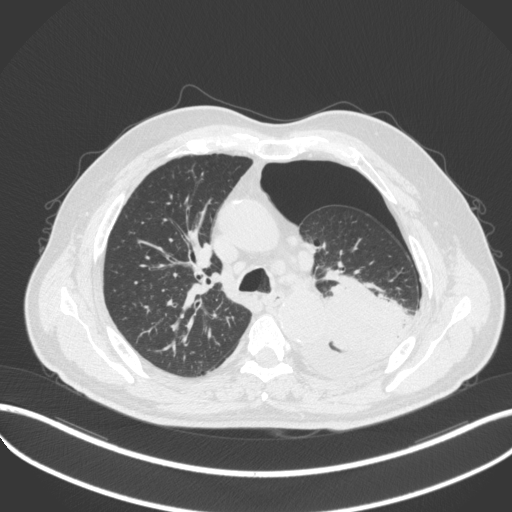
Chest CT, one axial slice. Position 348 of 466 along the scan axis. Reconstruction kernel B31f. 120 kVp. Lung window (W 1500 / L -600 HU). 512 × 512 image matrix, field of view 400 × 400 mm. Patient: male, 76 years. Case-level facts recorded for this patient, not image findings: clinical TNM (as recorded): T3 N0 M1b.
Outlined on this slice (bounding box drawn by a radiologist):
- lung tumour (recorded histology: adenocarcinoma): bounding box <298,267,416,388> (left, top, right, bottom; pixels)